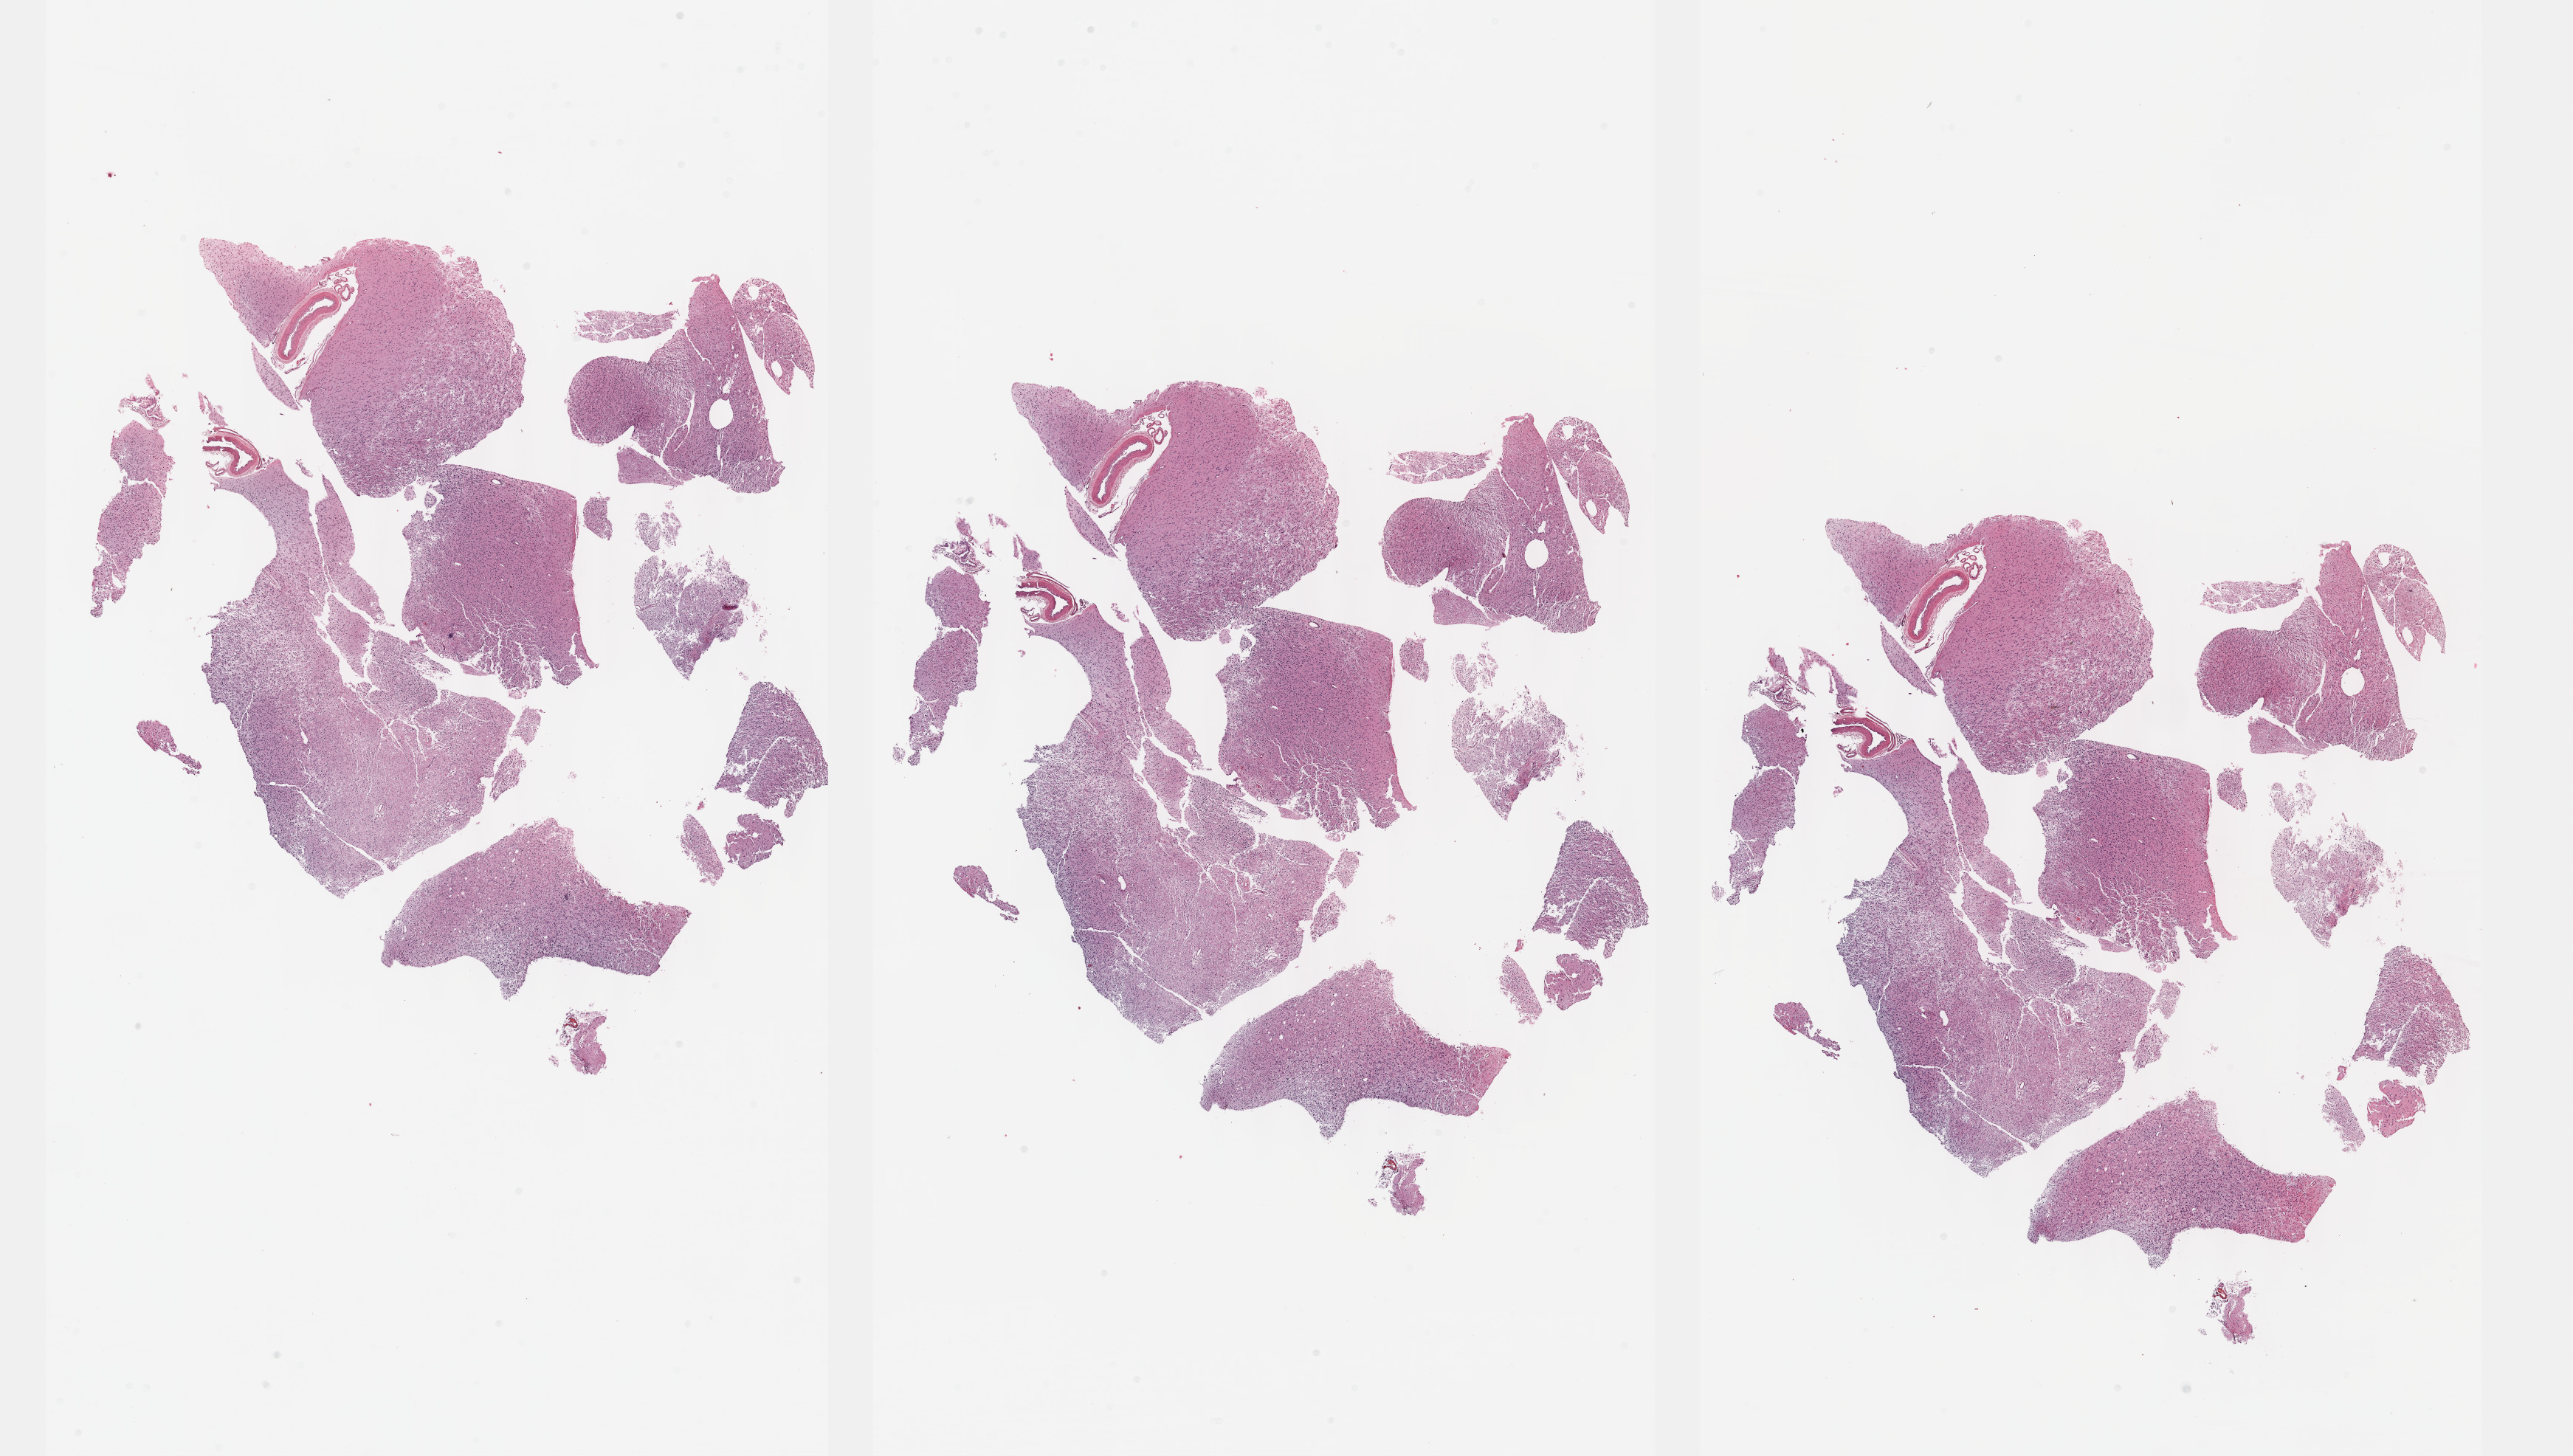
Hematoxylin and eosin (H&E) stained whole-slide image — a low-resolution overview of the entire scanned area, about 28.2 x 15.9 mm (acquisition: 40x scan). FFPE section. Primary tumour sample from the brain. Female, age 53 years at initial diagnosis.
Diagnosis: Oligodendroglioma, anaplastic (cerebrum).